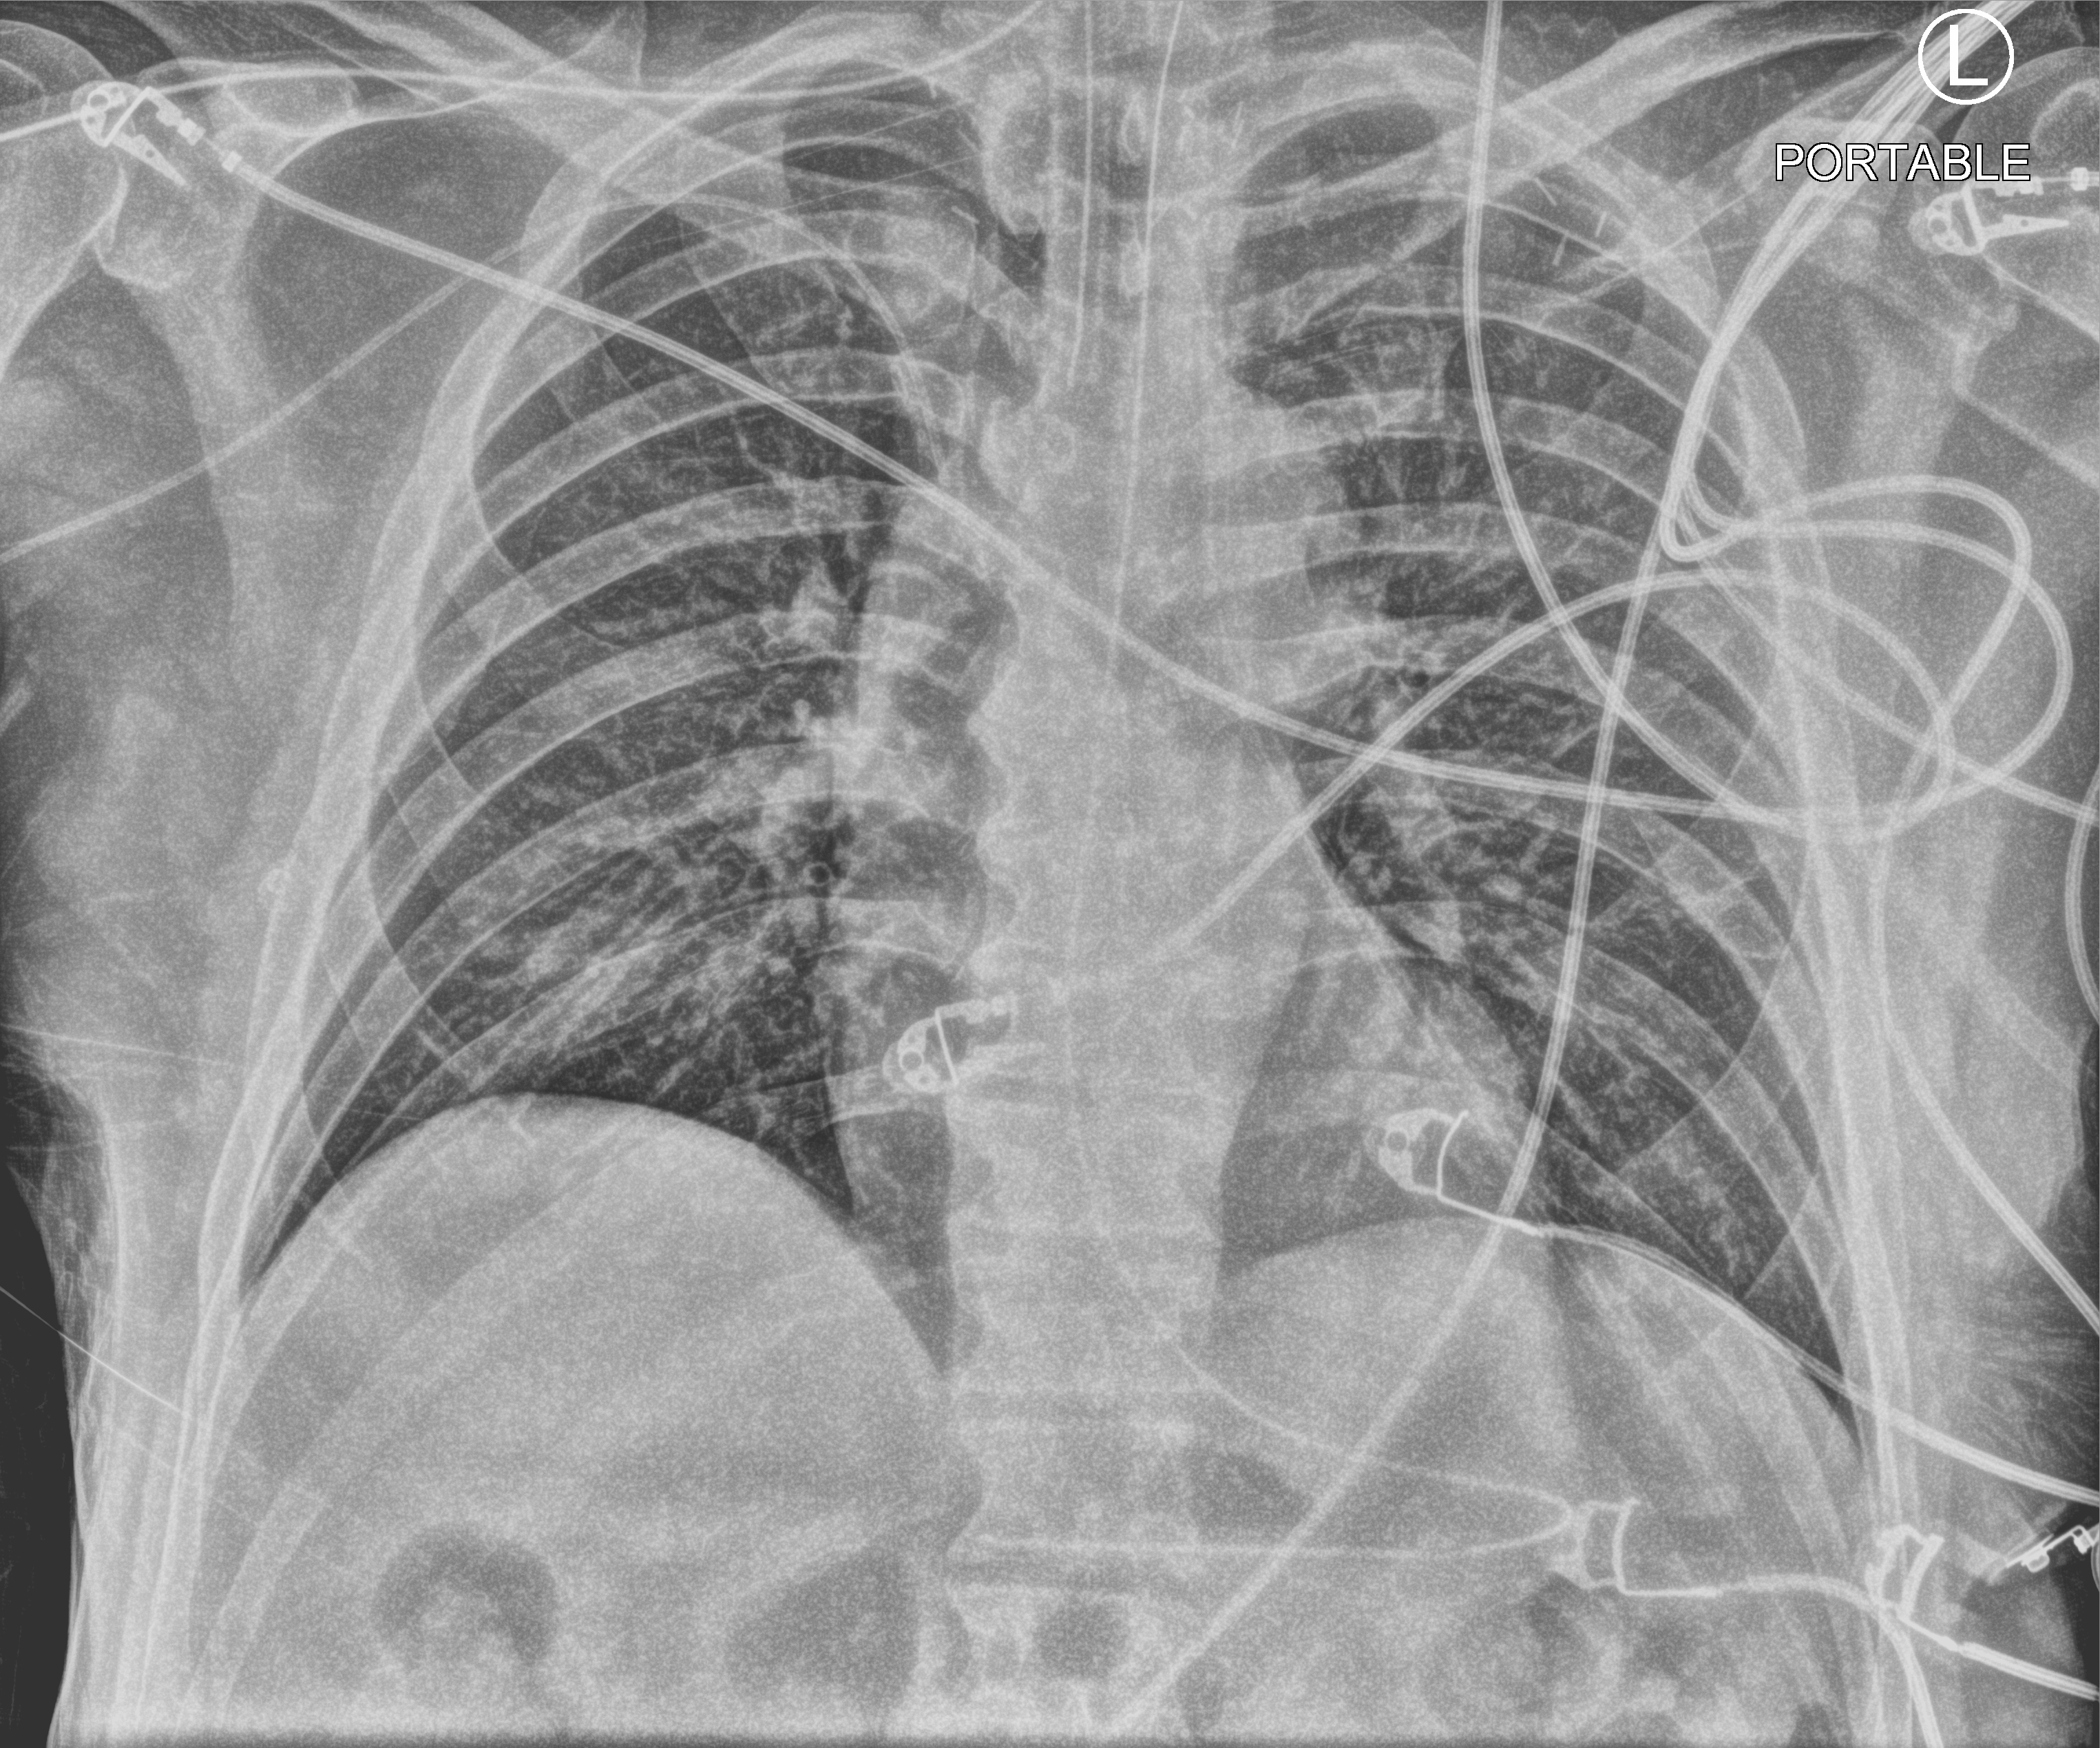
Chest X-ray (portable); anteroposterior (AP) projection. Patient hospitalised with COVID-19, aged 18–59 years.
Hospital-stay facts (about this admission, not read from this image; timing relative to this image not recorded): admitted to intensive care during this hospital stay: yes.